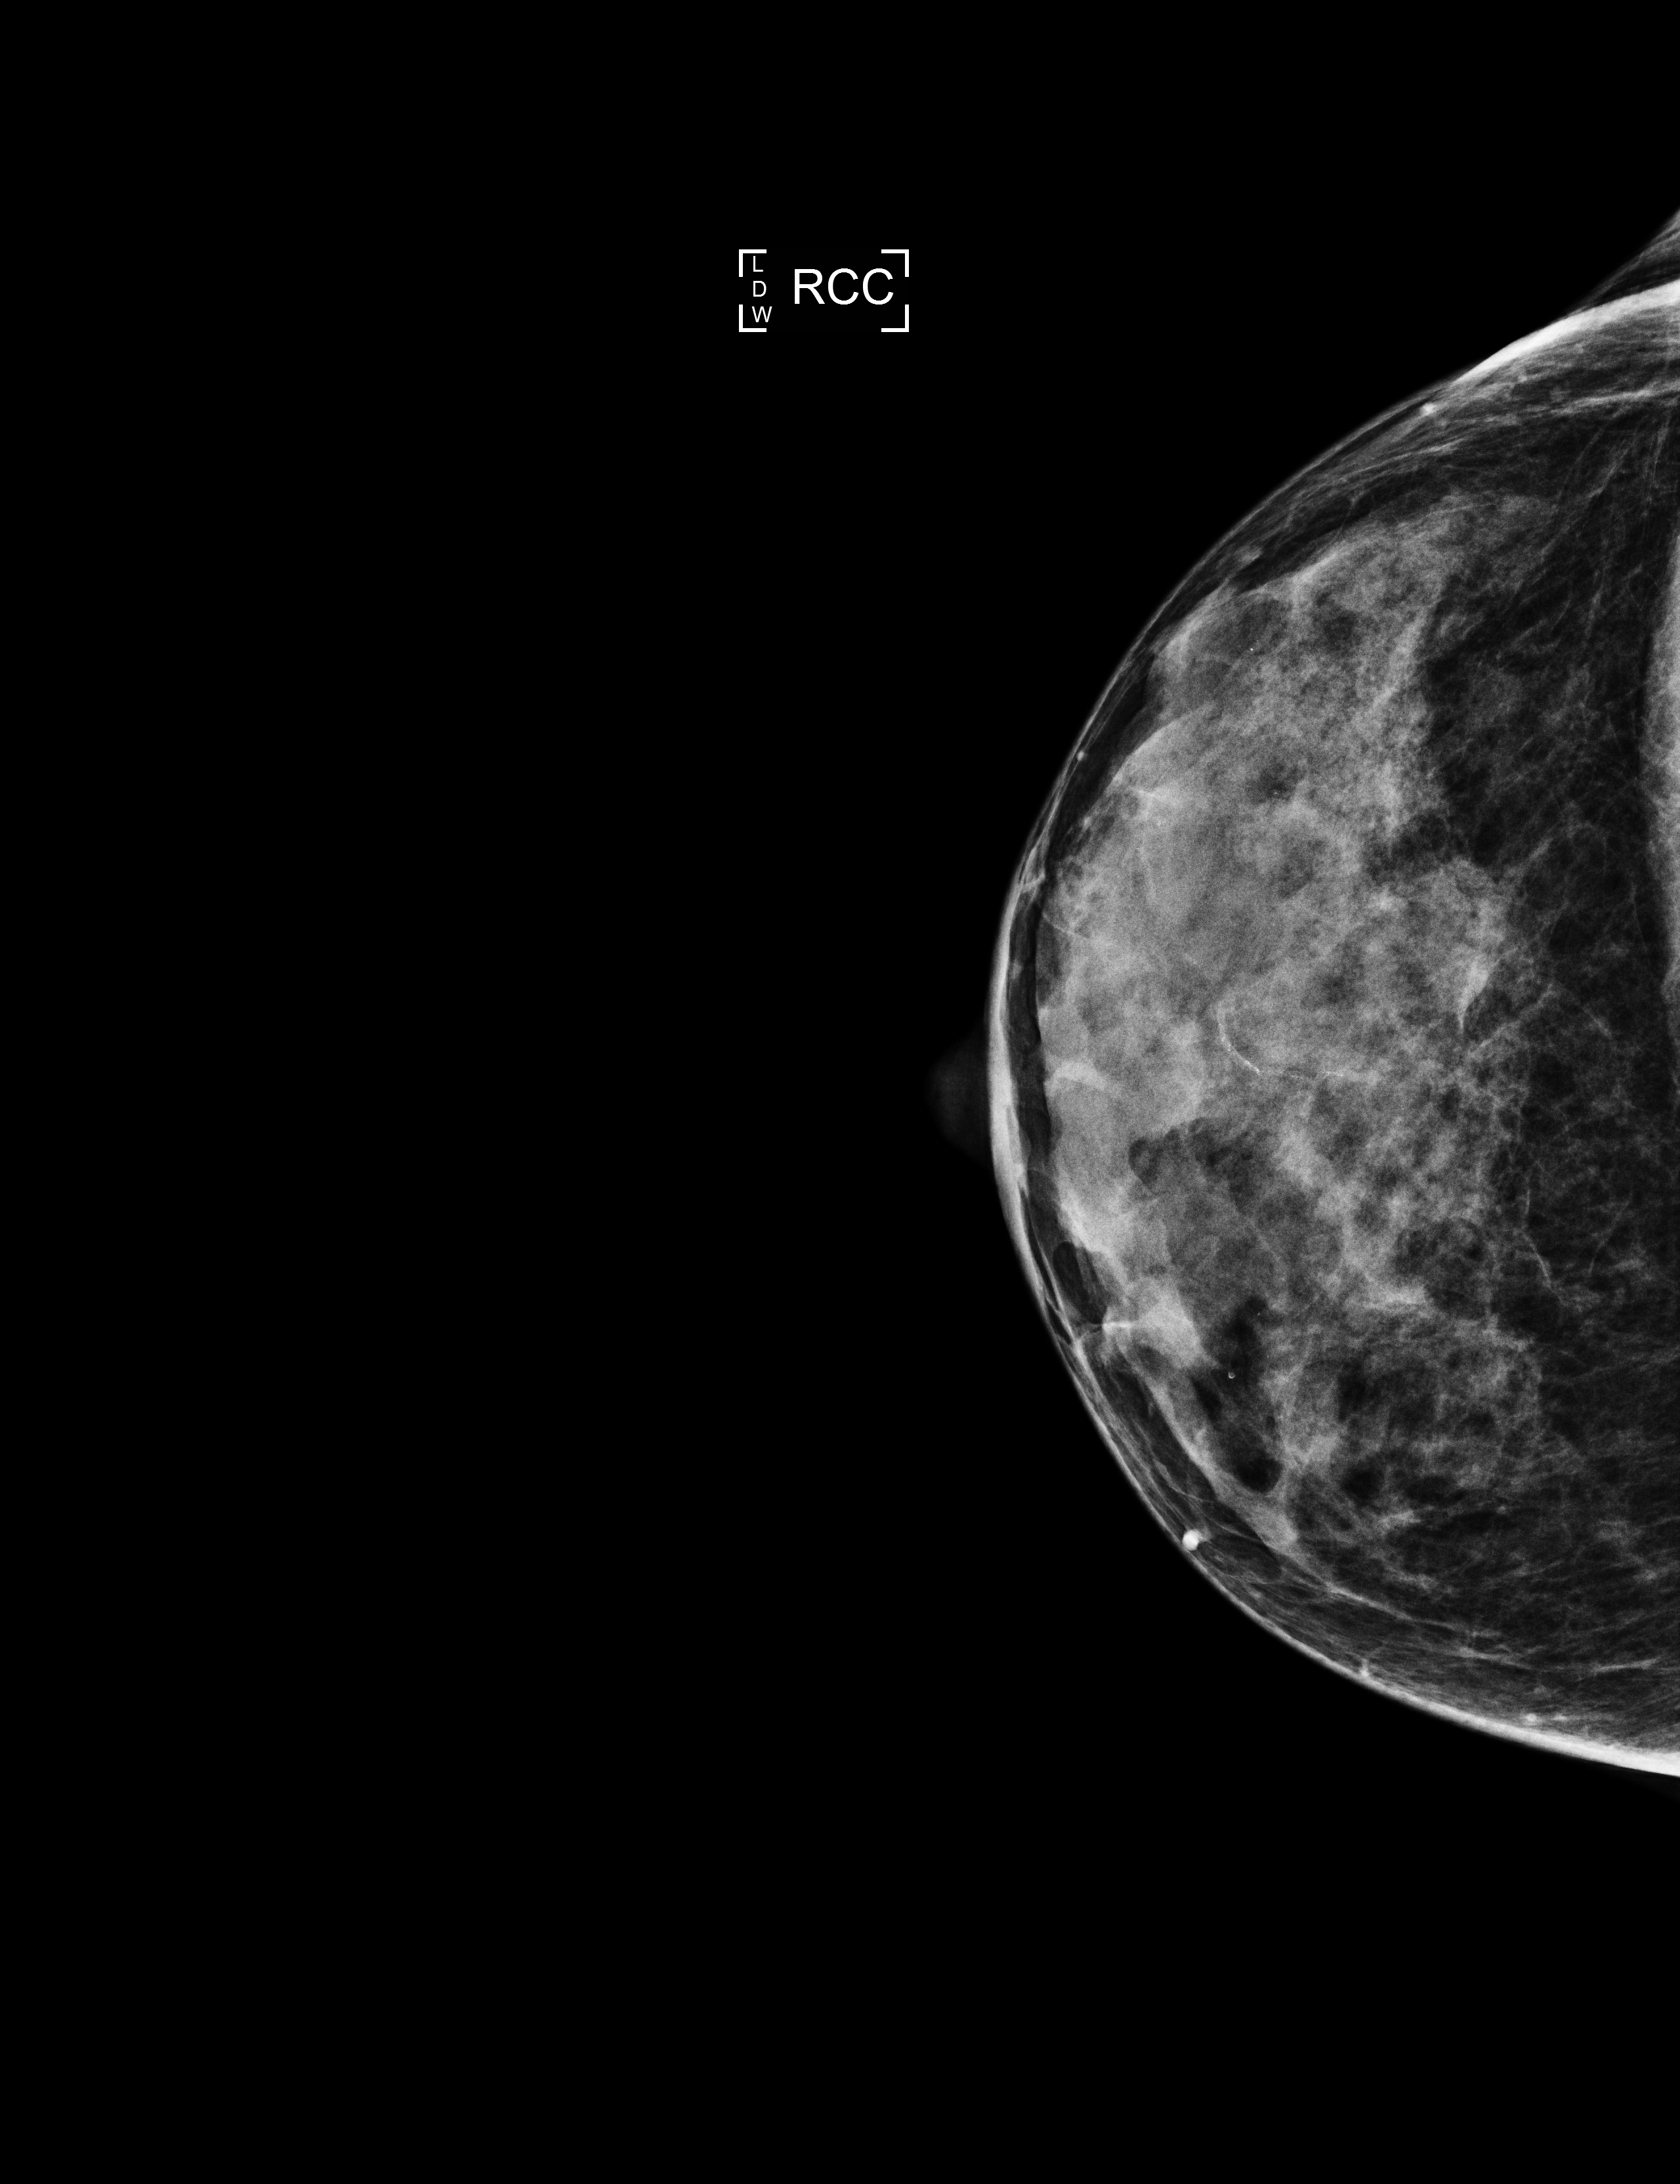
Screening examination; compressed breast thickness 36 mm; system: Selenia Dimensions. Patient aged 58 years (female).
Image type: full-field digital mammogram. Breast: right. Projection: craniocaudal (CC) view.